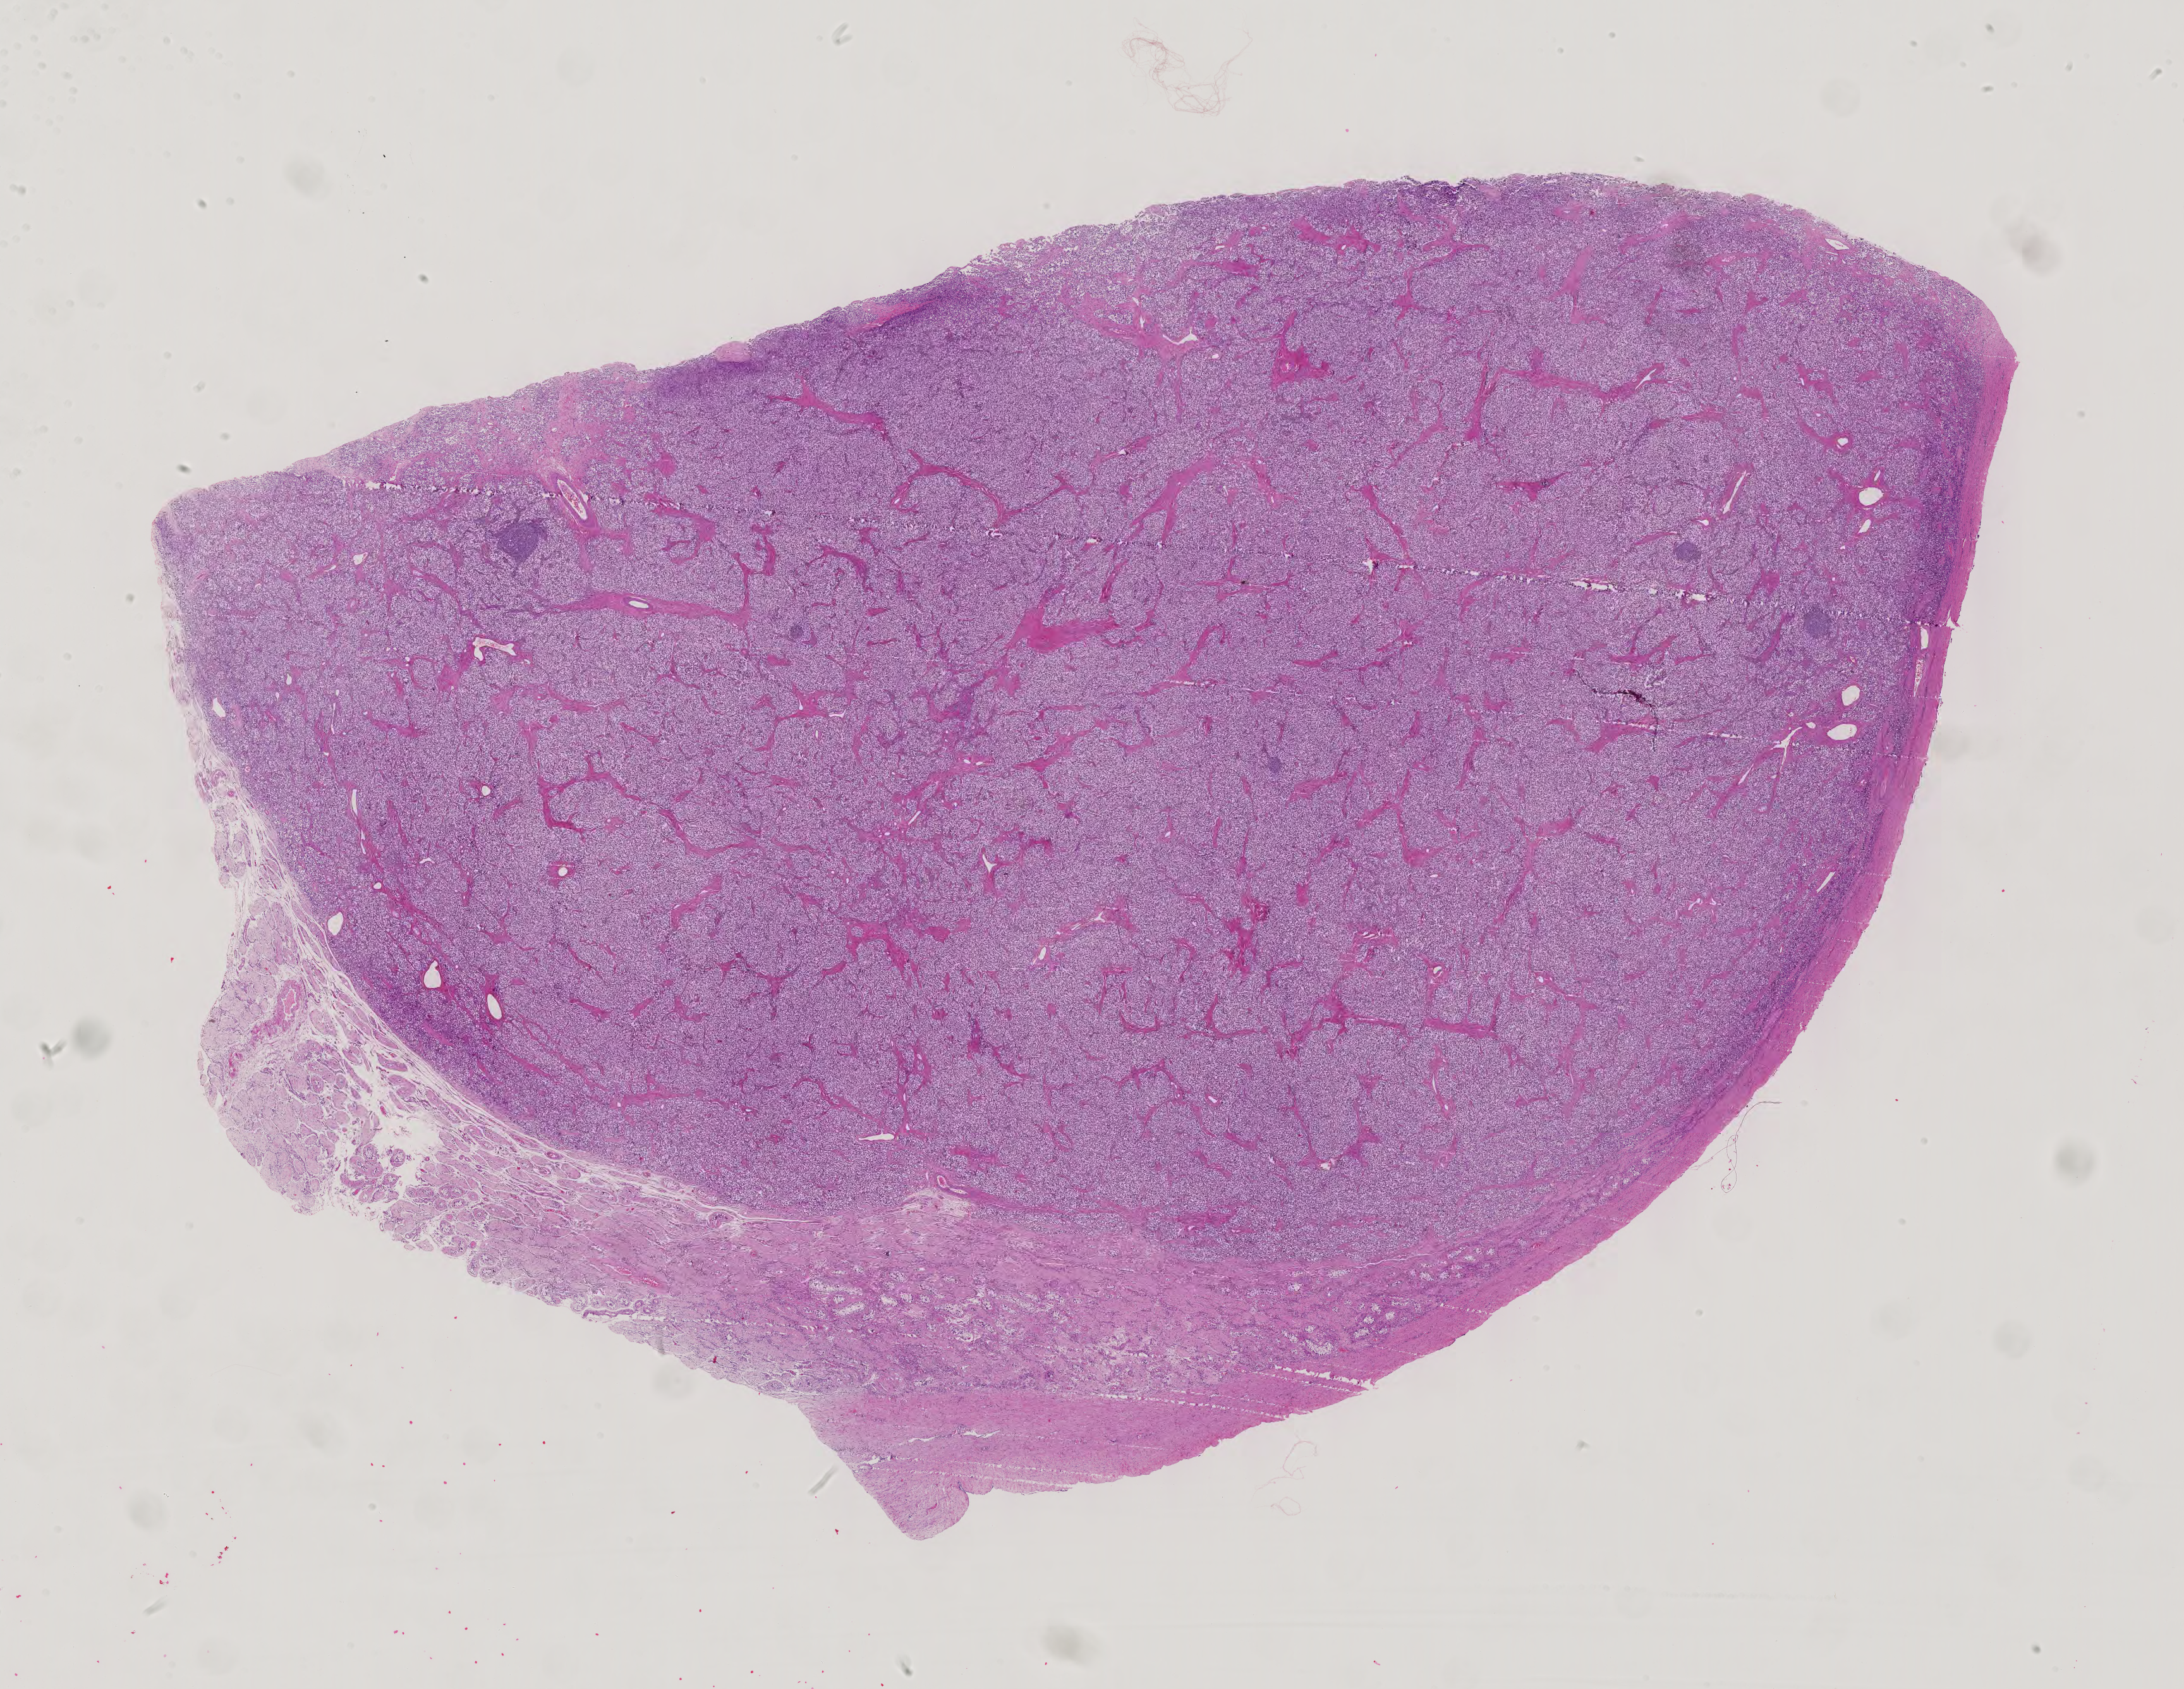
Digitized H&E tissue section (whole slide) — shown as a low-resolution overview of the whole scanned area (about 25.2 x 19.5 mm, slide scanned at 40x), formalin-fixed paraffin-embedded (FFPE) diagnostic section, primary tumour sample from the testis. Male, age 30 years at initial diagnosis.
Histologic diagnosis: Seminoma, NOS.